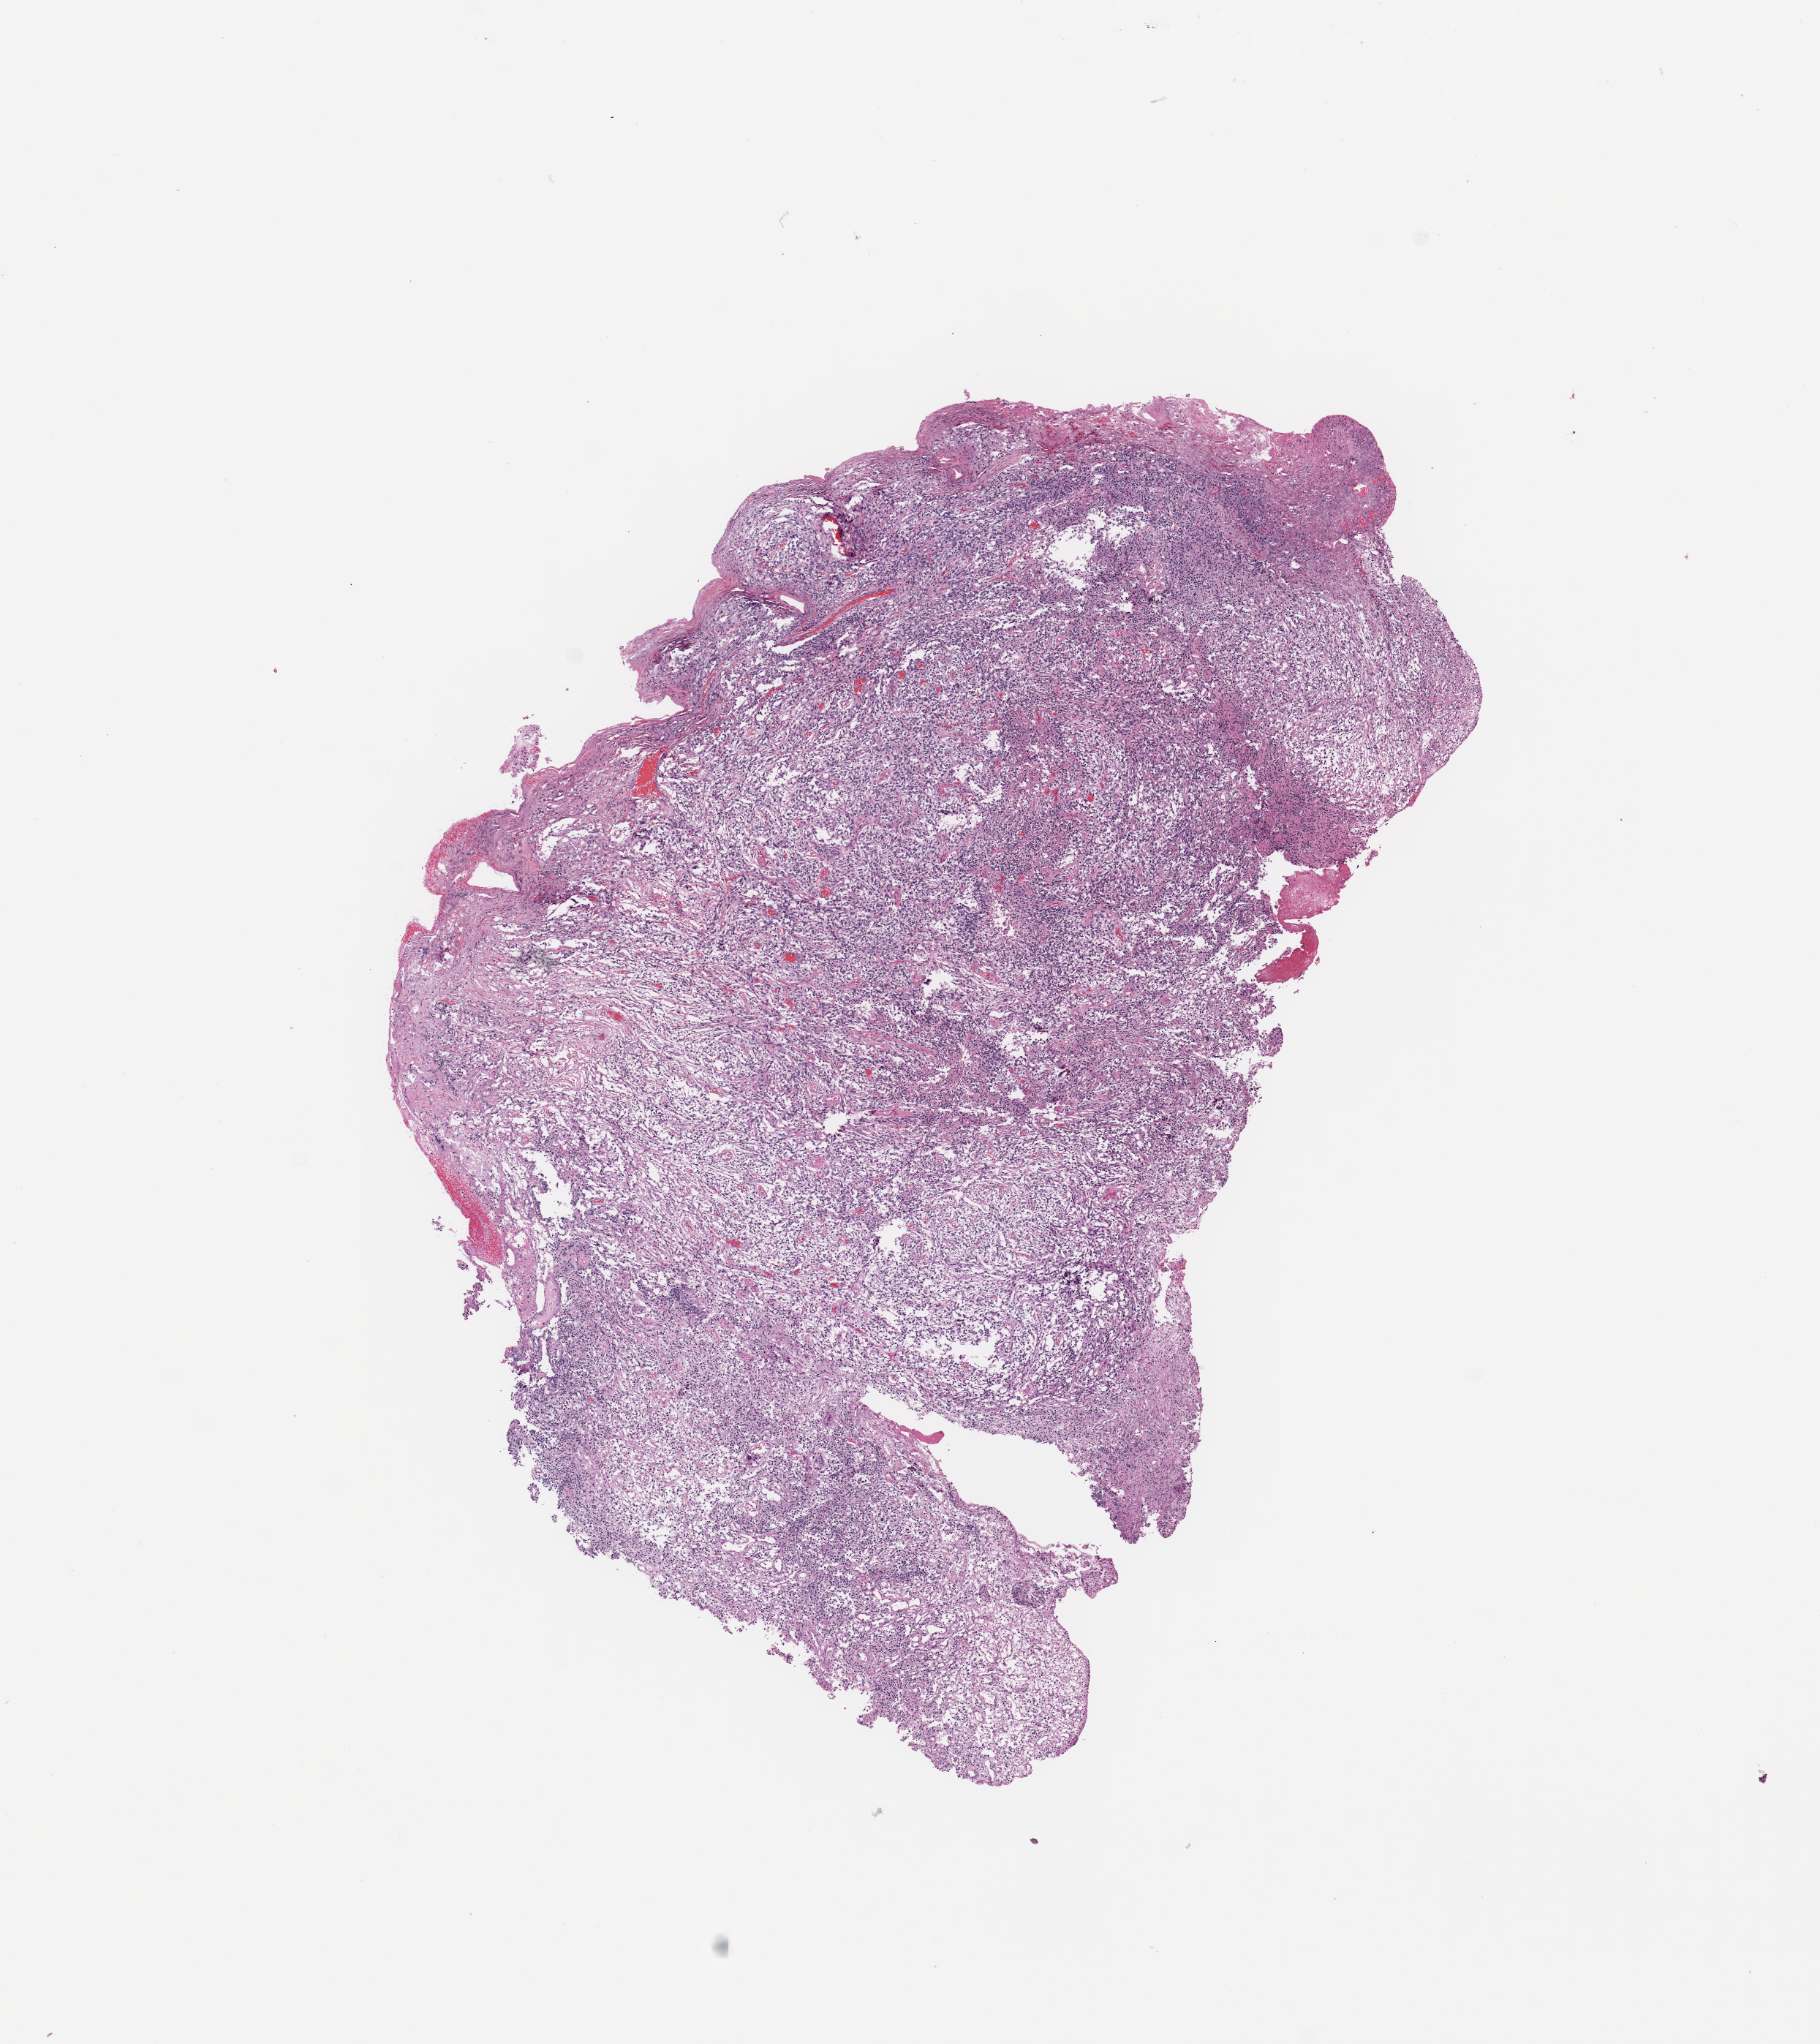
Whole-slide histology image, H&E-stained — shown as a low-resolution overview of the whole scanned area (about 9.8 x 11.1 mm, acquisition: 20x scan), tumour tissue sample, sampled site: temporal cortex. Female, 73 y/o. Pathologist review of this section (percent, as recorded): tumour nuclei 85%, necrosis 3%.
Histologic diagnosis: Glioblastoma.